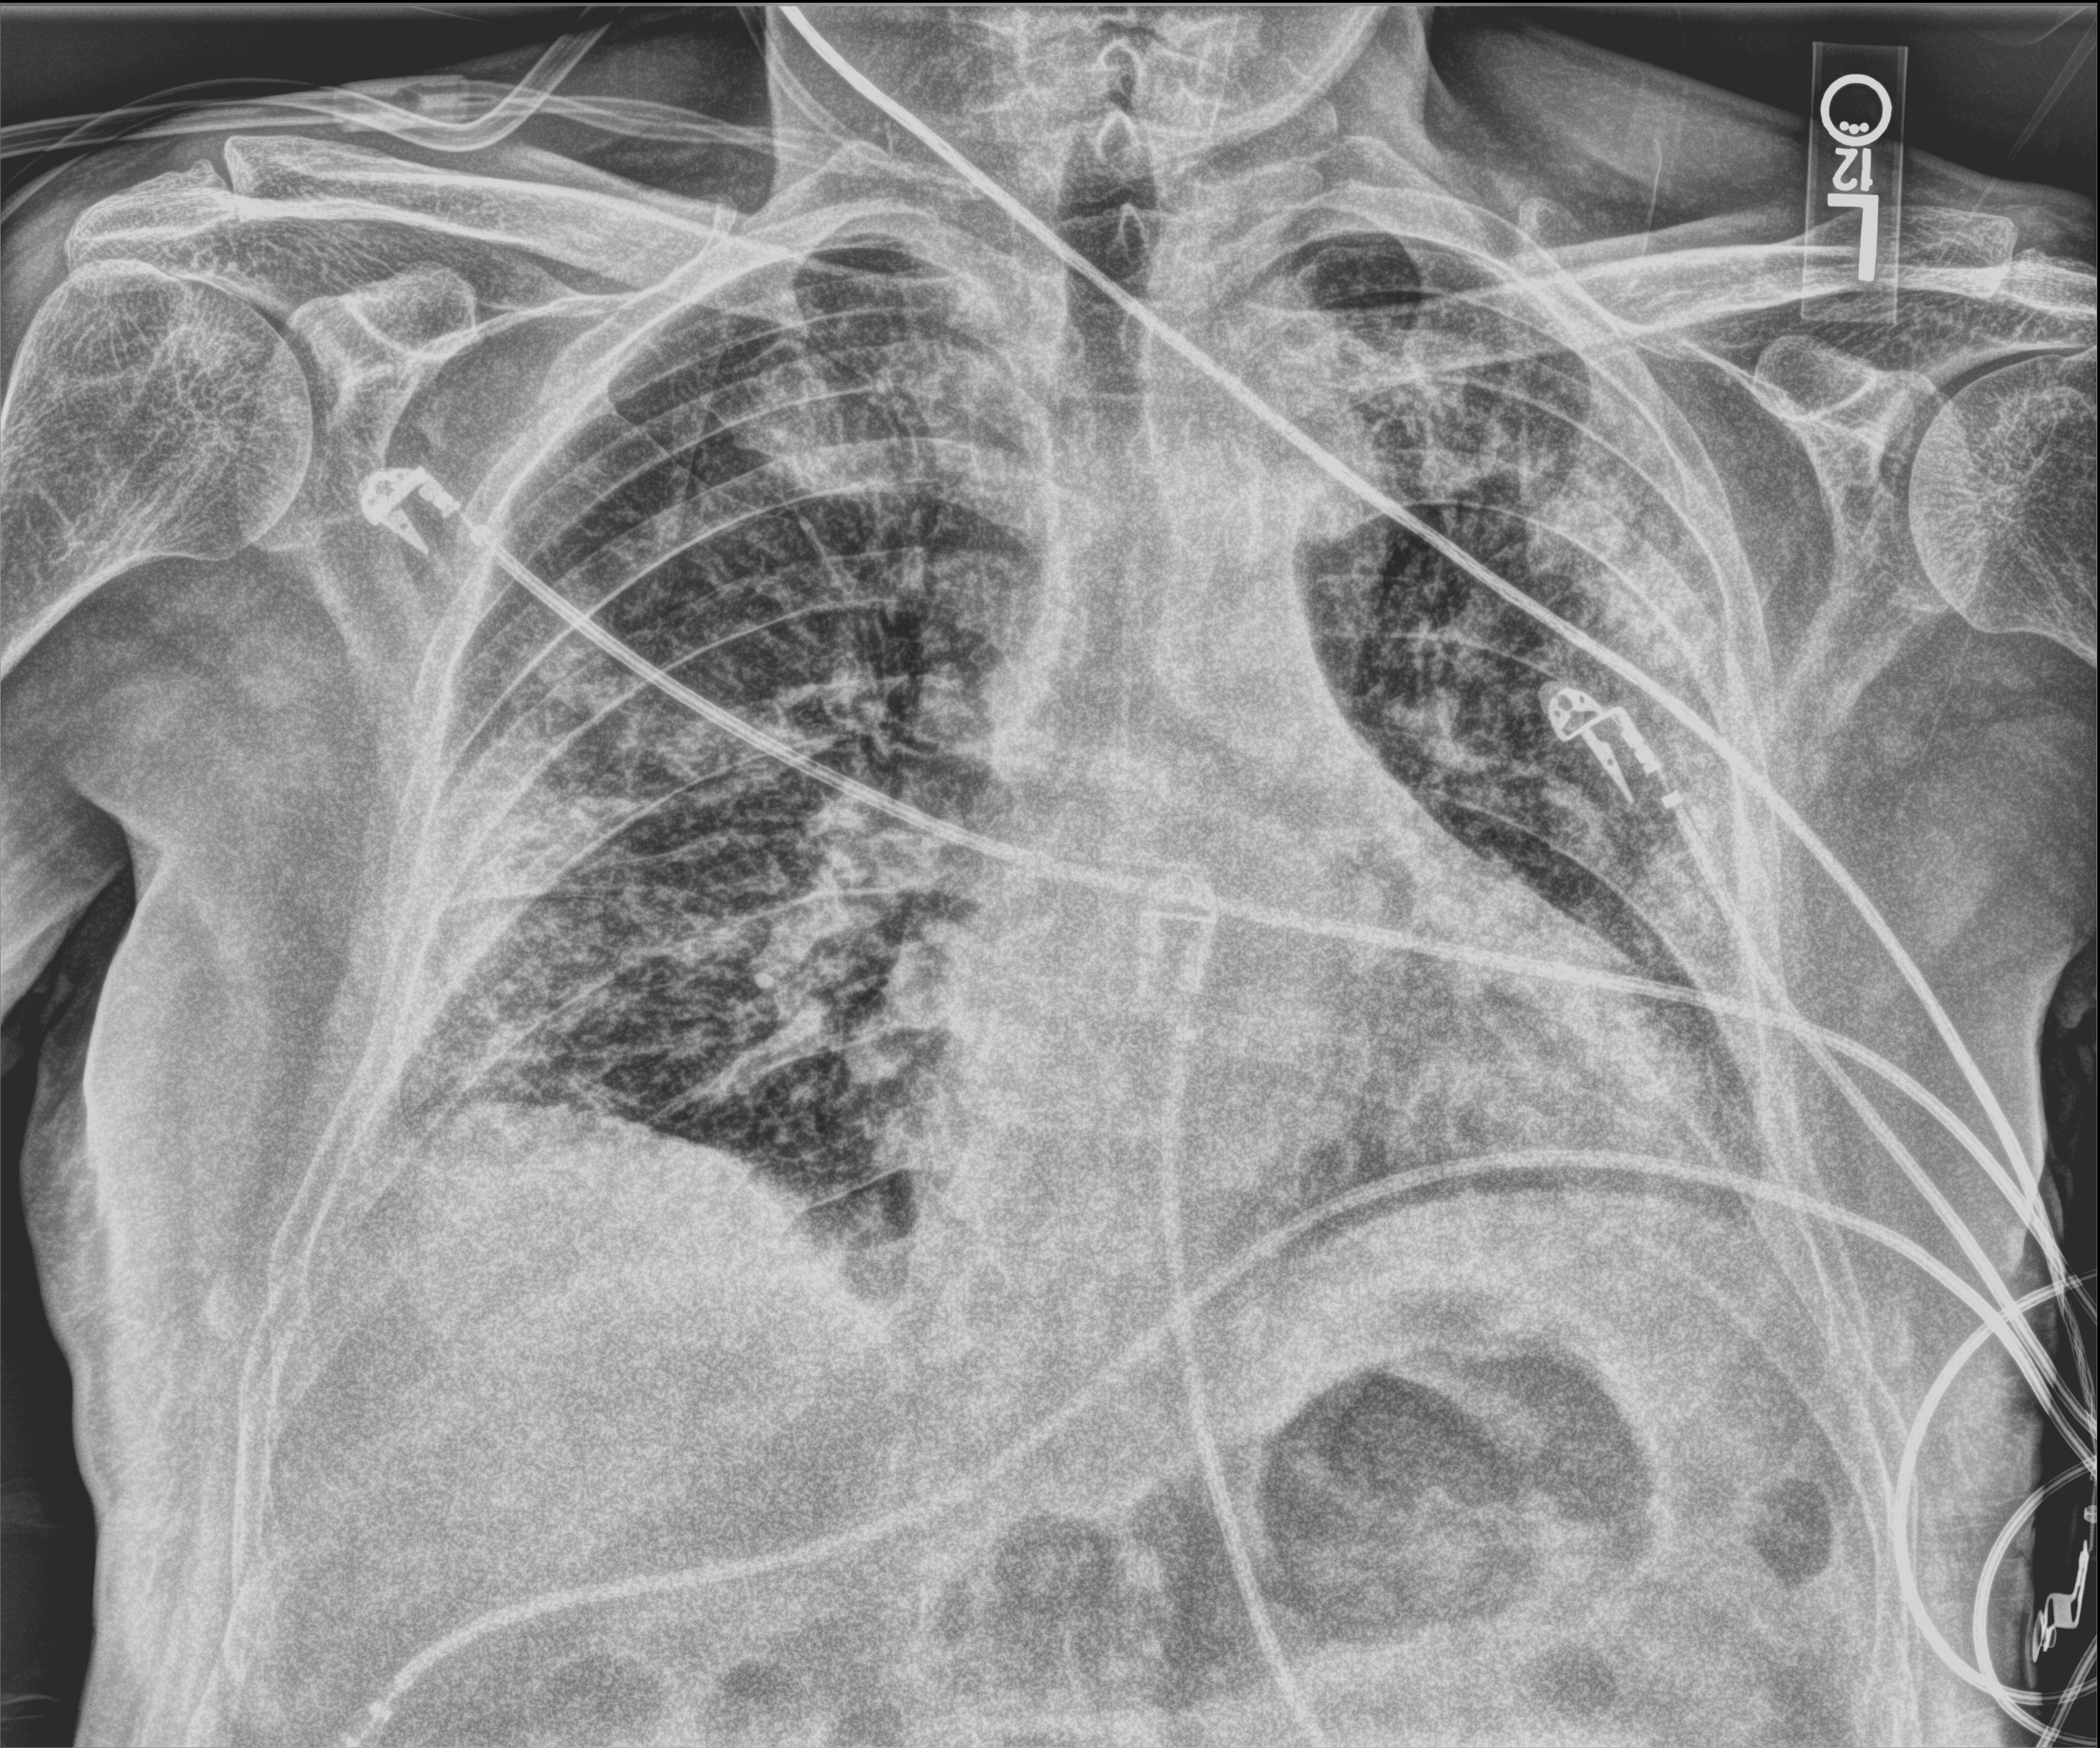
Portable chest radiograph, anteroposterior (AP) projection. Male patient hospitalised with COVID-19, age 60–74 years.
From the hospital-stay record, not from the radiograph (when in the stay this image was taken is not recorded):
- mechanically ventilated during this hospital stay: no